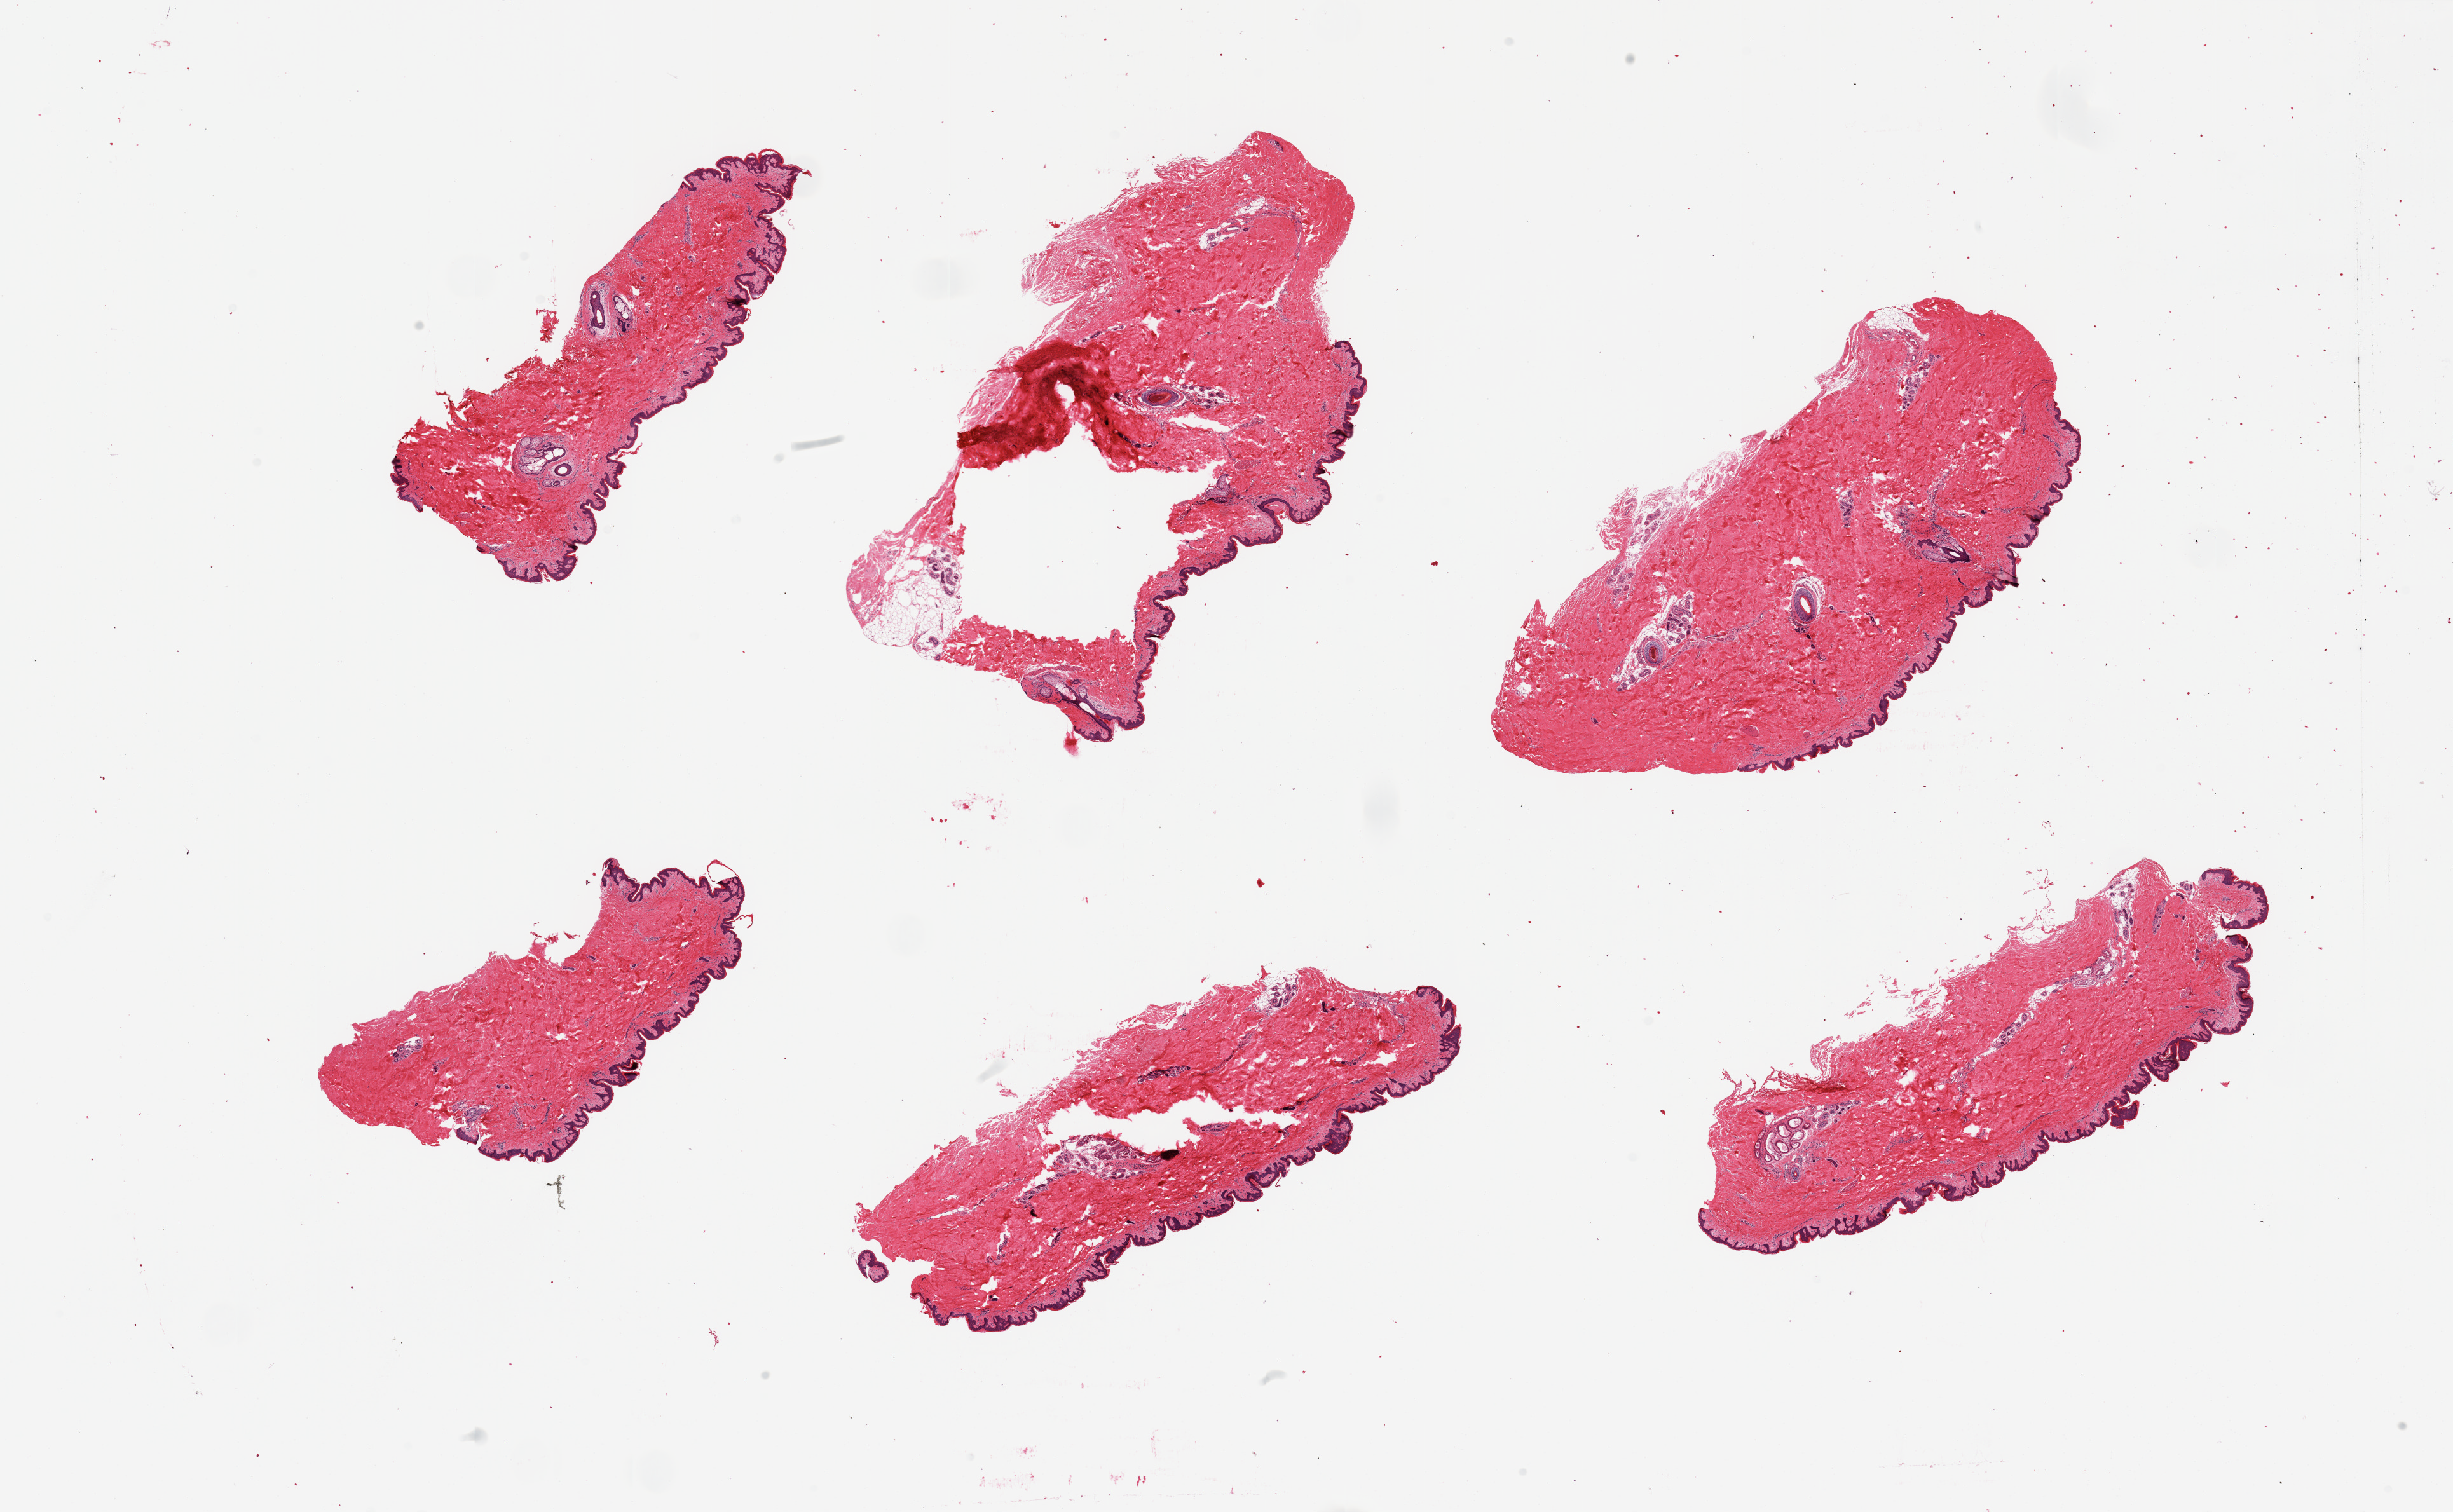
Whole-slide image, H&E stain — shown as a low-resolution overview of the whole scanned area (about 30.5 x 18.8 mm, acquisition: 20x scan); PAXgene-fixed paraffin-embedded (PFPE) section; section of skin of suprapubic region (target tissue); donor tissue sample. Male donor.
* reviewer comment on this tissue sample: 6 pieces; well trimmed of fat